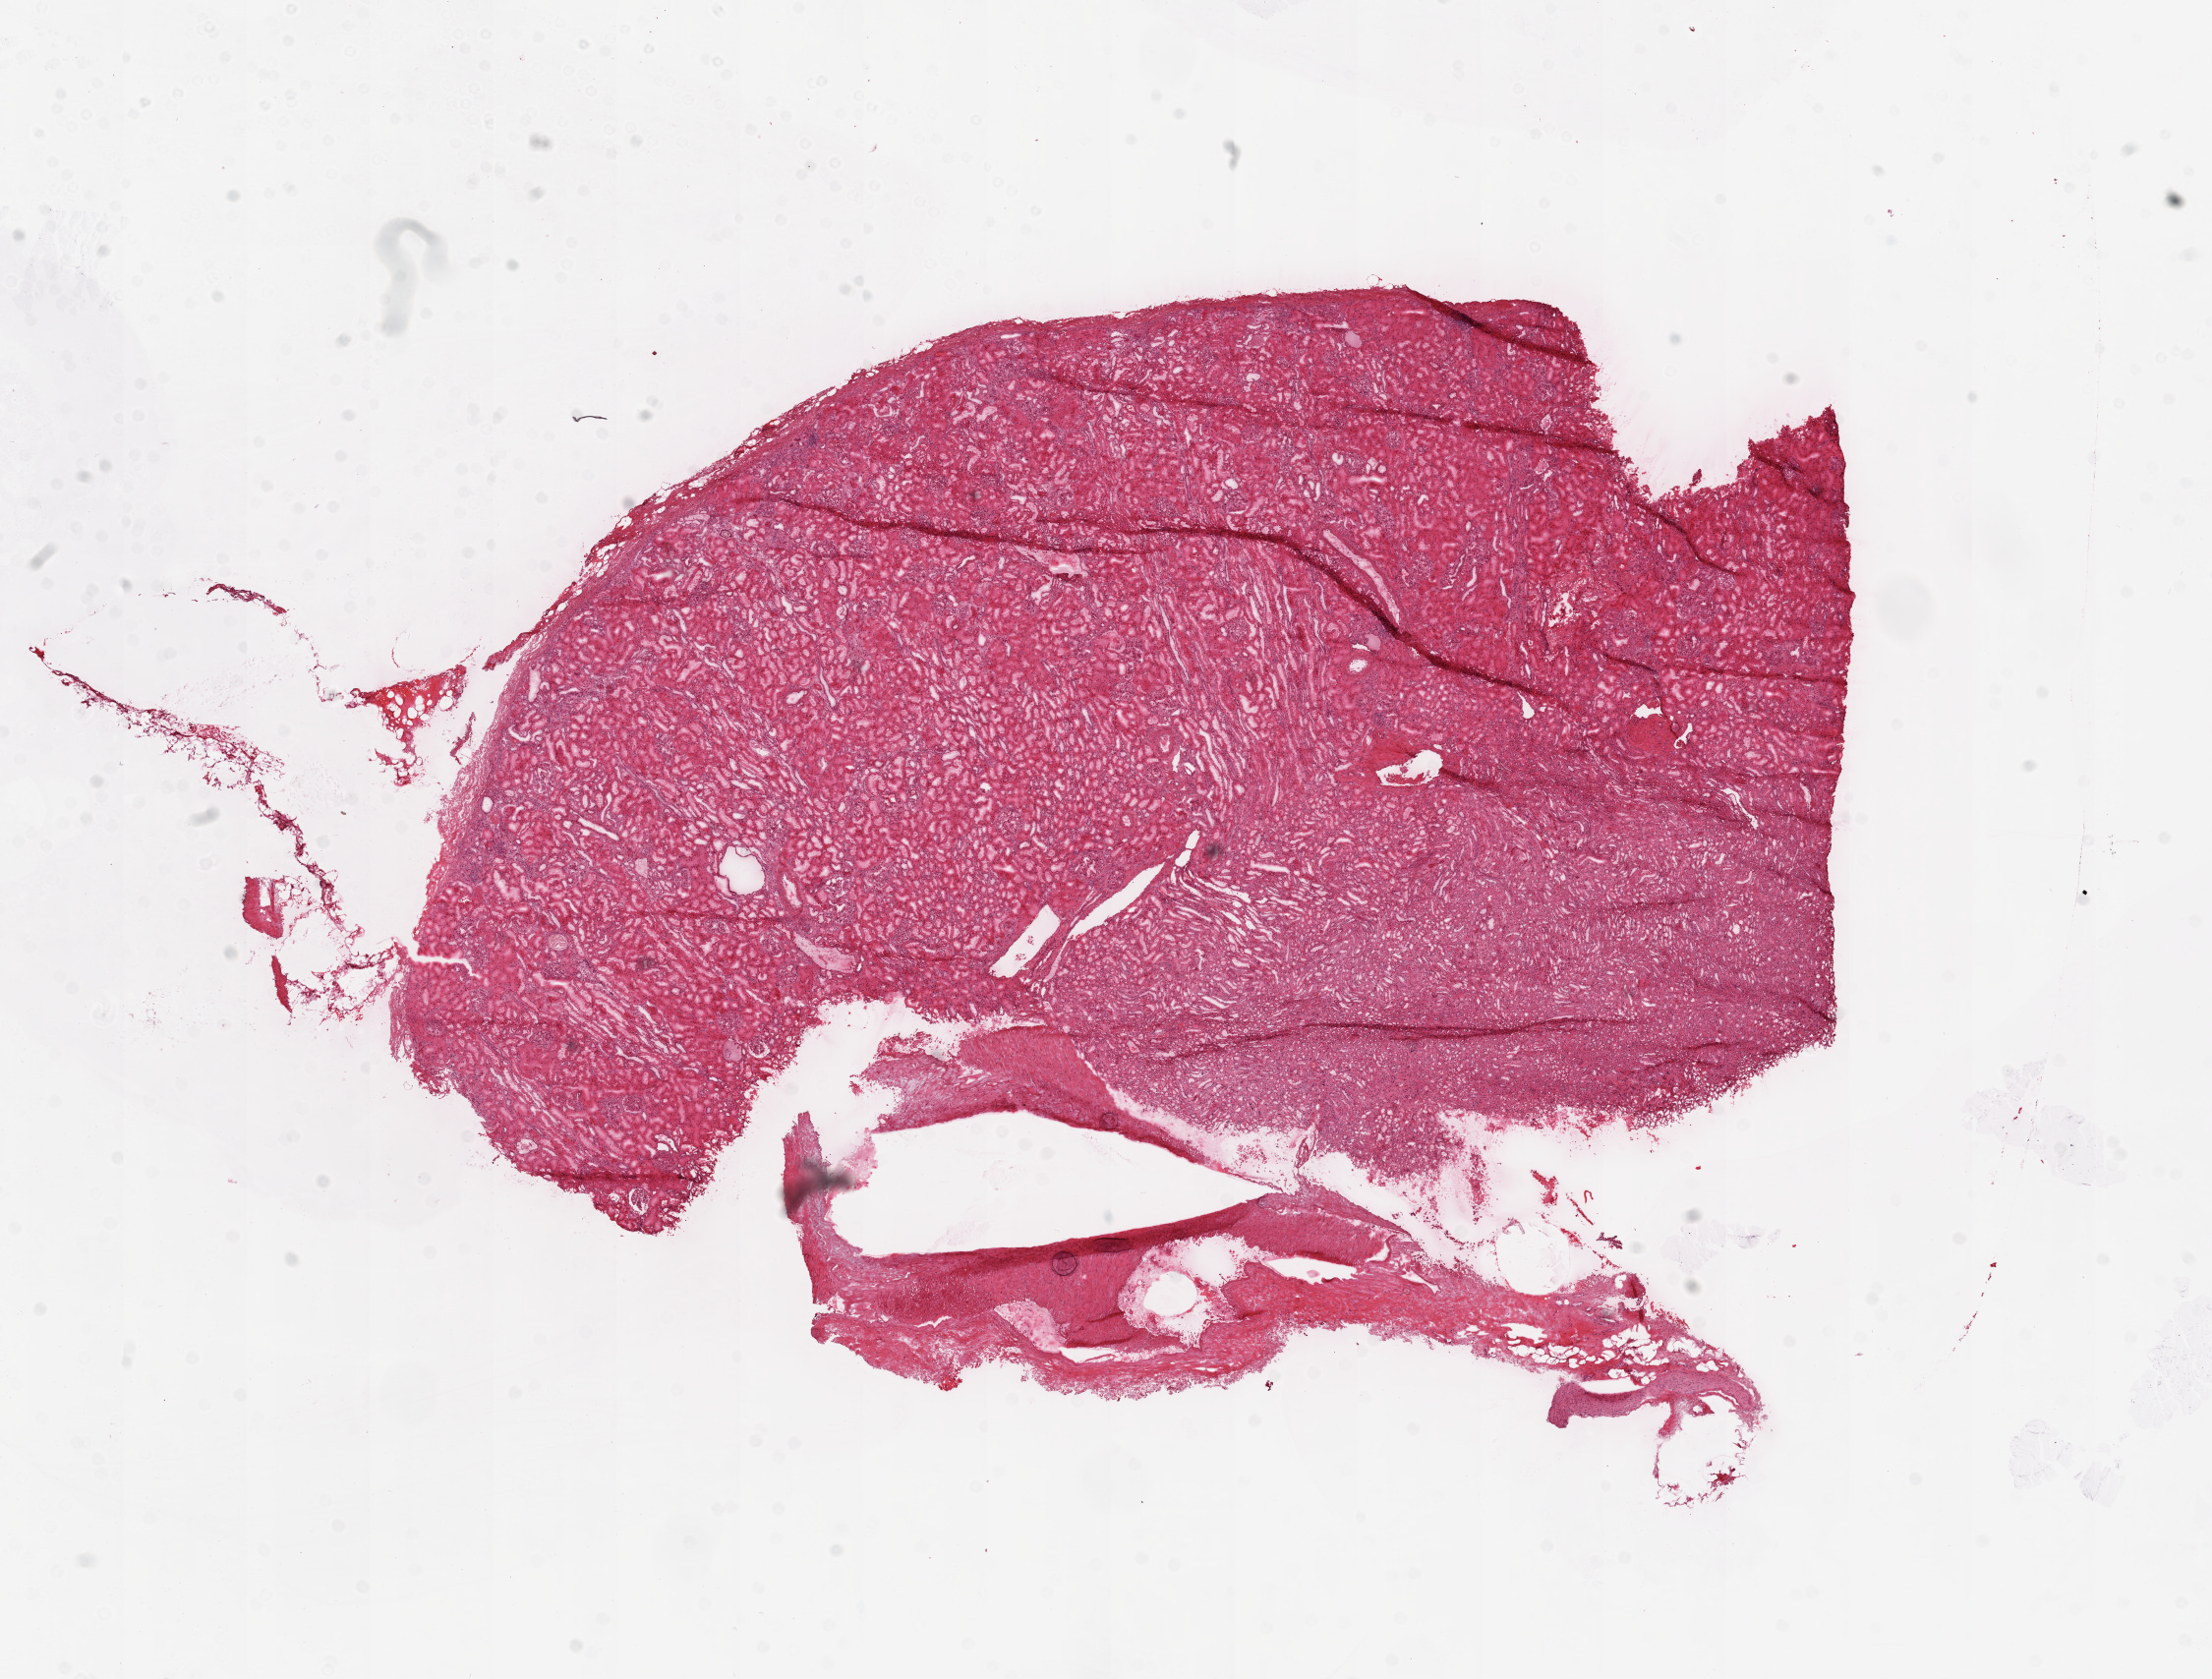
H&E-stained whole-slide image, shown as a low-resolution overview of the whole scanned area (about 18.1 x 13.7 mm), frozen section from the top of the tissue portion, solid tissue normal (non-tumour tissue) sample from the kidney. Female patient; age at initial diagnosis 67 years.
This section: solid tissue normal sample (biorepository sample class). Patient diagnosis: Clear cell adenocarcinoma, NOS.